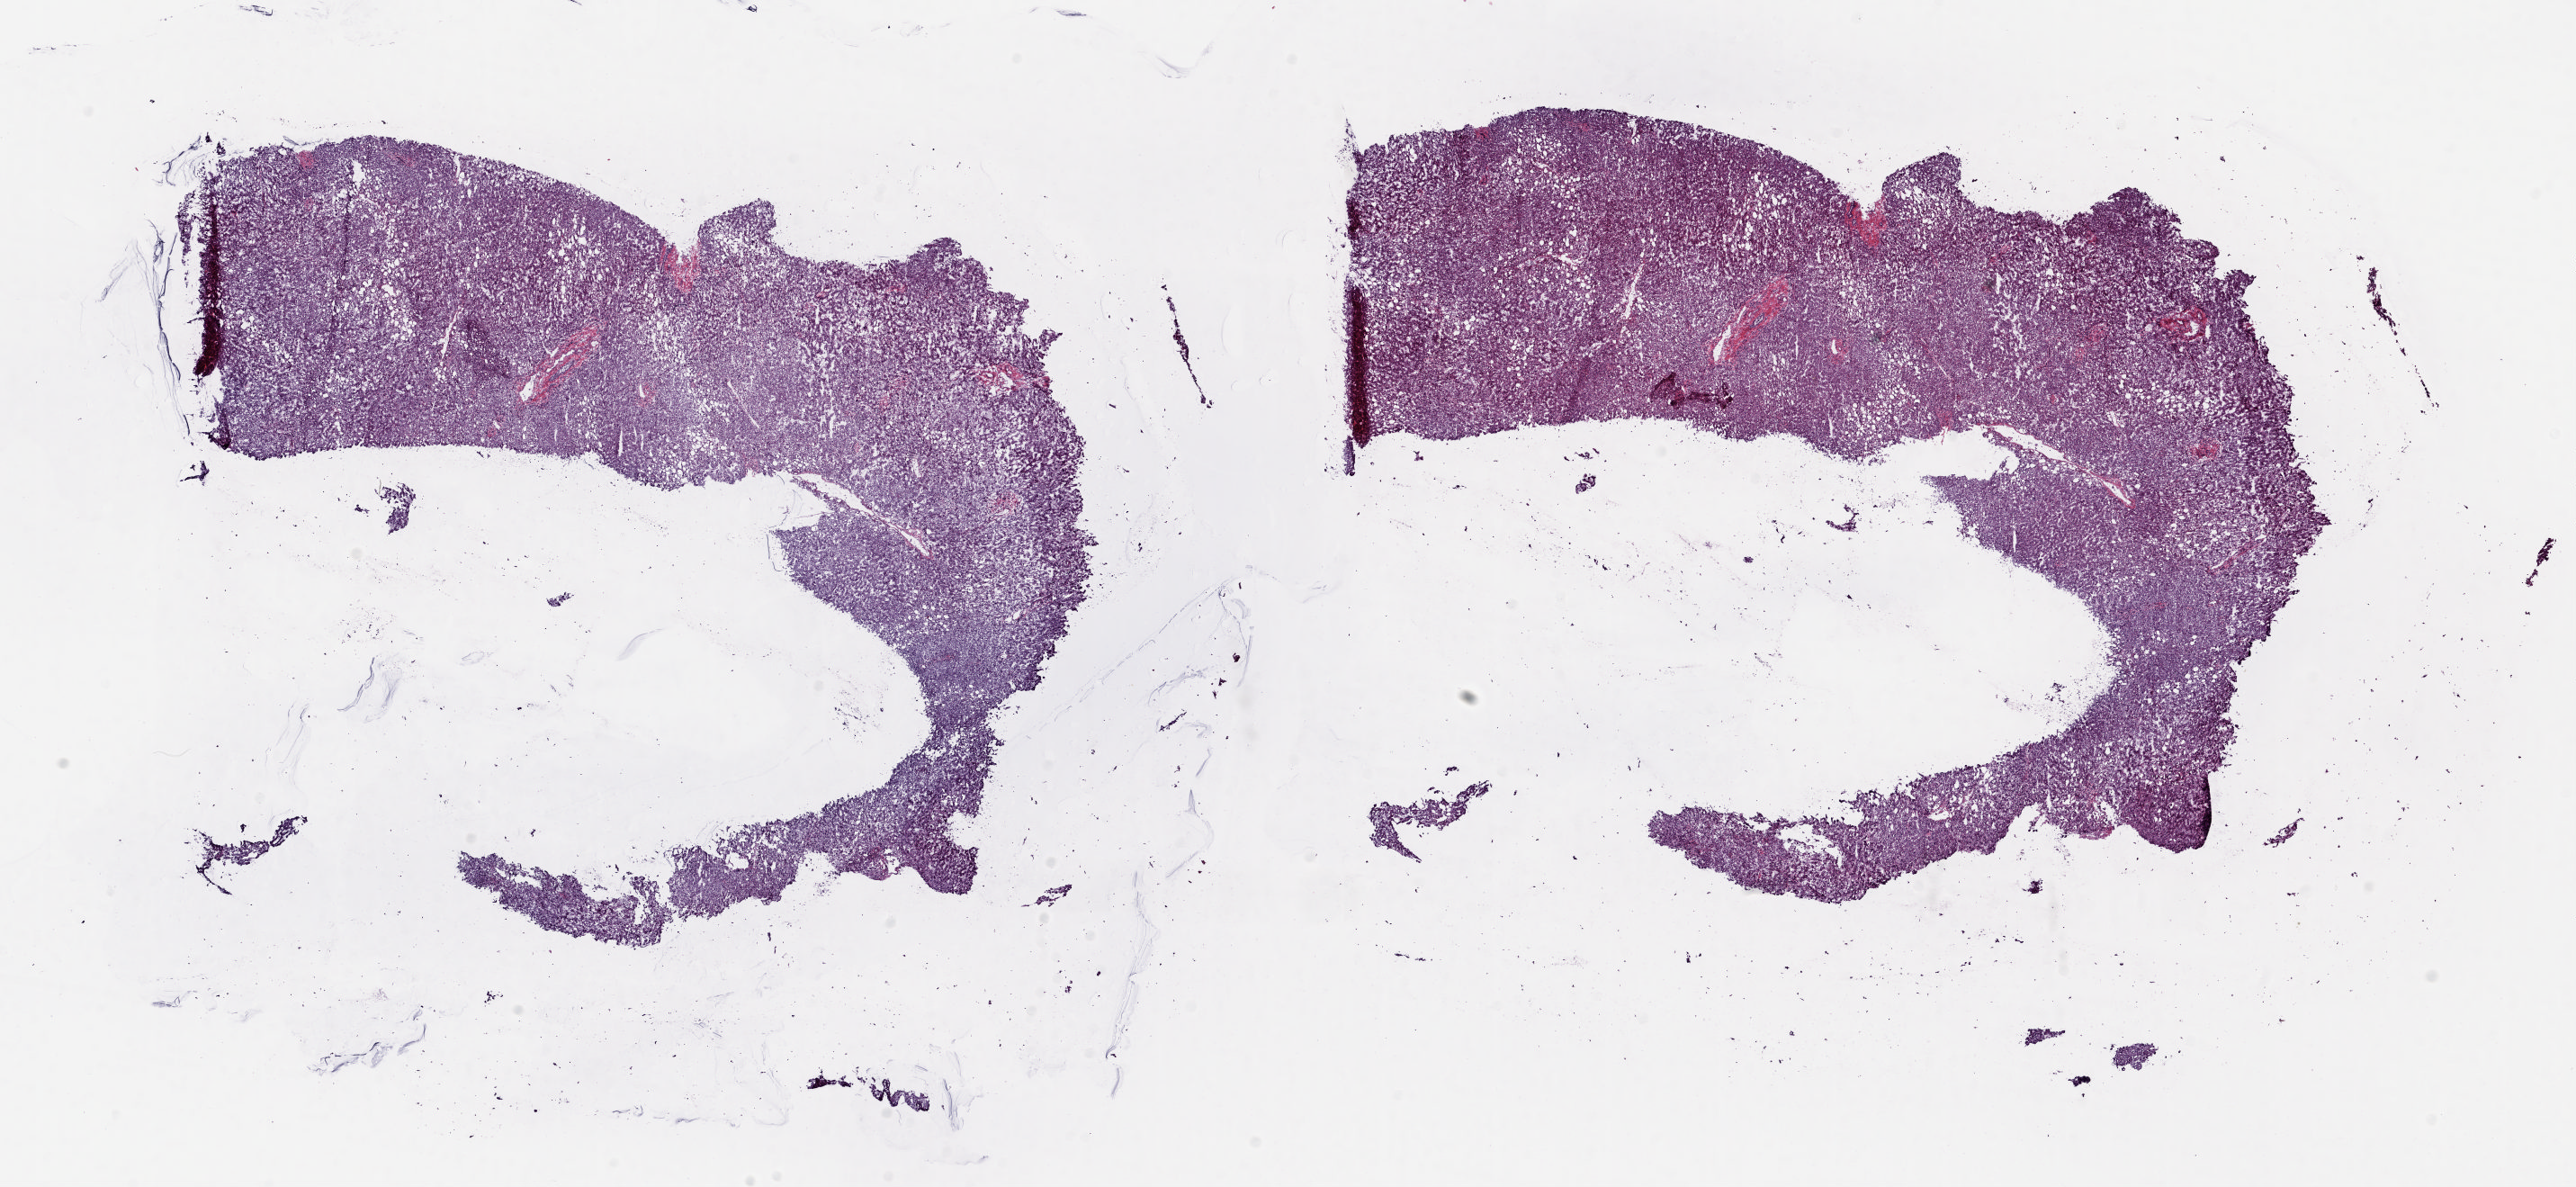
Whole-slide histology image, H&E-stained — low-resolution overview of the scanned area, about 22.7 x 10.5 mm (slide scanned at 20x); frozen section from the top of the tissue portion; liver, solid tissue normal (non-tumour tissue) sample. Patient: male, age at initial diagnosis 69 years. Composition of this section per pathologist review: tumour cells 0%, tumour nuclei 0%, normal cells 100%, stromal cells 0%, necrosis 0%. Infiltration values recorded for this section: lymphocyte infiltration 0%, monocyte infiltration 0%, neutrophil infiltration 0%.
This section: solid tissue normal (non-tumour) sample from the same patient. Patient diagnosis: Hepatocellular carcinoma, NOS.